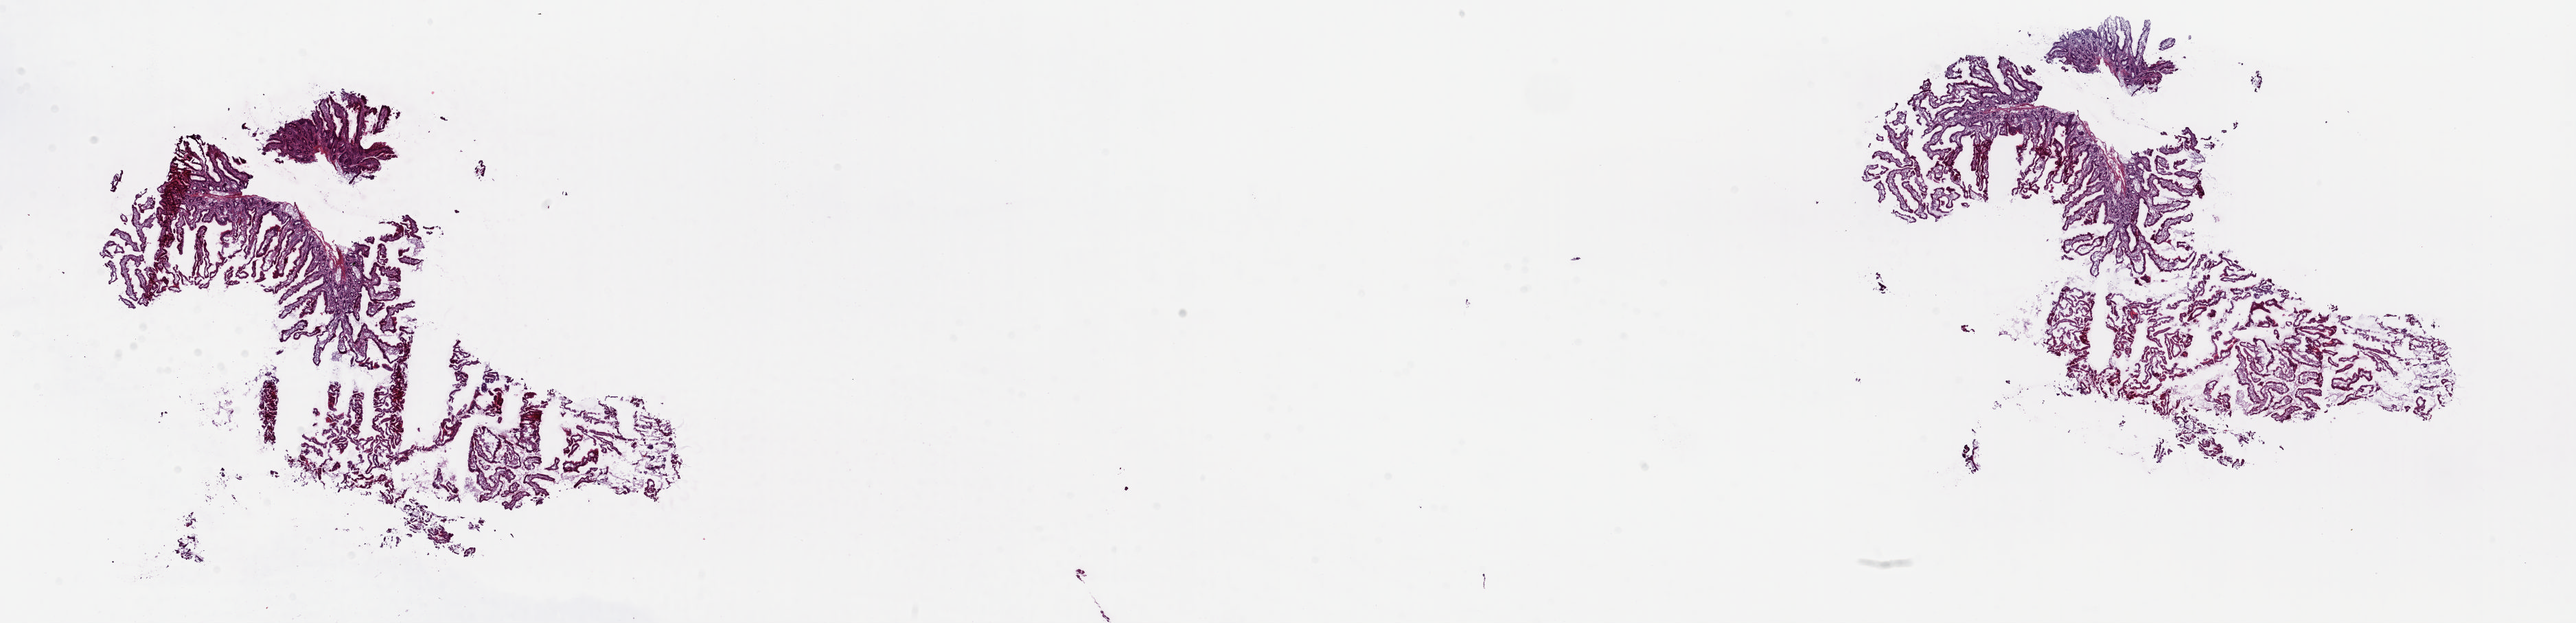
Digitized Hematoxylin and eosin (H&E) stained tissue section (whole slide) — whole scanned area (about 29.8 x 7.2 mm, from a 20x scan) shown as a low-resolution overview, frozen section, solid tissue normal (non-tumour tissue) sample from the pancreas. Female, age 57 years at initial diagnosis. Pathologist review of this section (percent, as recorded): tumour cells 0%, tumour nuclei 0%, normal cells 100%, stromal cells 0%, necrosis 0%. Inflammatory infiltration, as recorded: lymphocyte infiltration 2%, monocyte infiltration 0%, neutrophil infiltration 0%.
• this section: solid tissue normal (non-tumour) sample from the same patient
• patient diagnosis: Infiltrating duct carcinoma, NOS (head of pancreas)